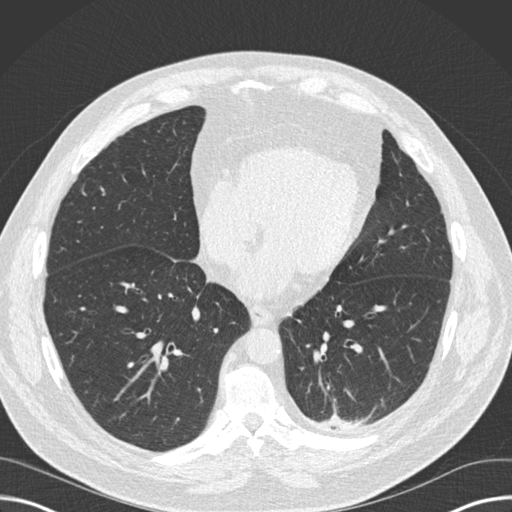
Low-dose screening chest CT, one axial slice. Slice 60 of 160 in the series (ordered by position). Reconstruction kernel B30f. 120 kVp. Lung window (W 1500 / L -600 HU). 512 × 512 image matrix, field of view 382 × 382 mm.
Structures marked on this image (outlined manually by an expert reader):
- lesion 1 (tumor, upper lobe of left lung): bounding box (x1, y1, x2, y2) in pixels: (324, 412, 364, 427)